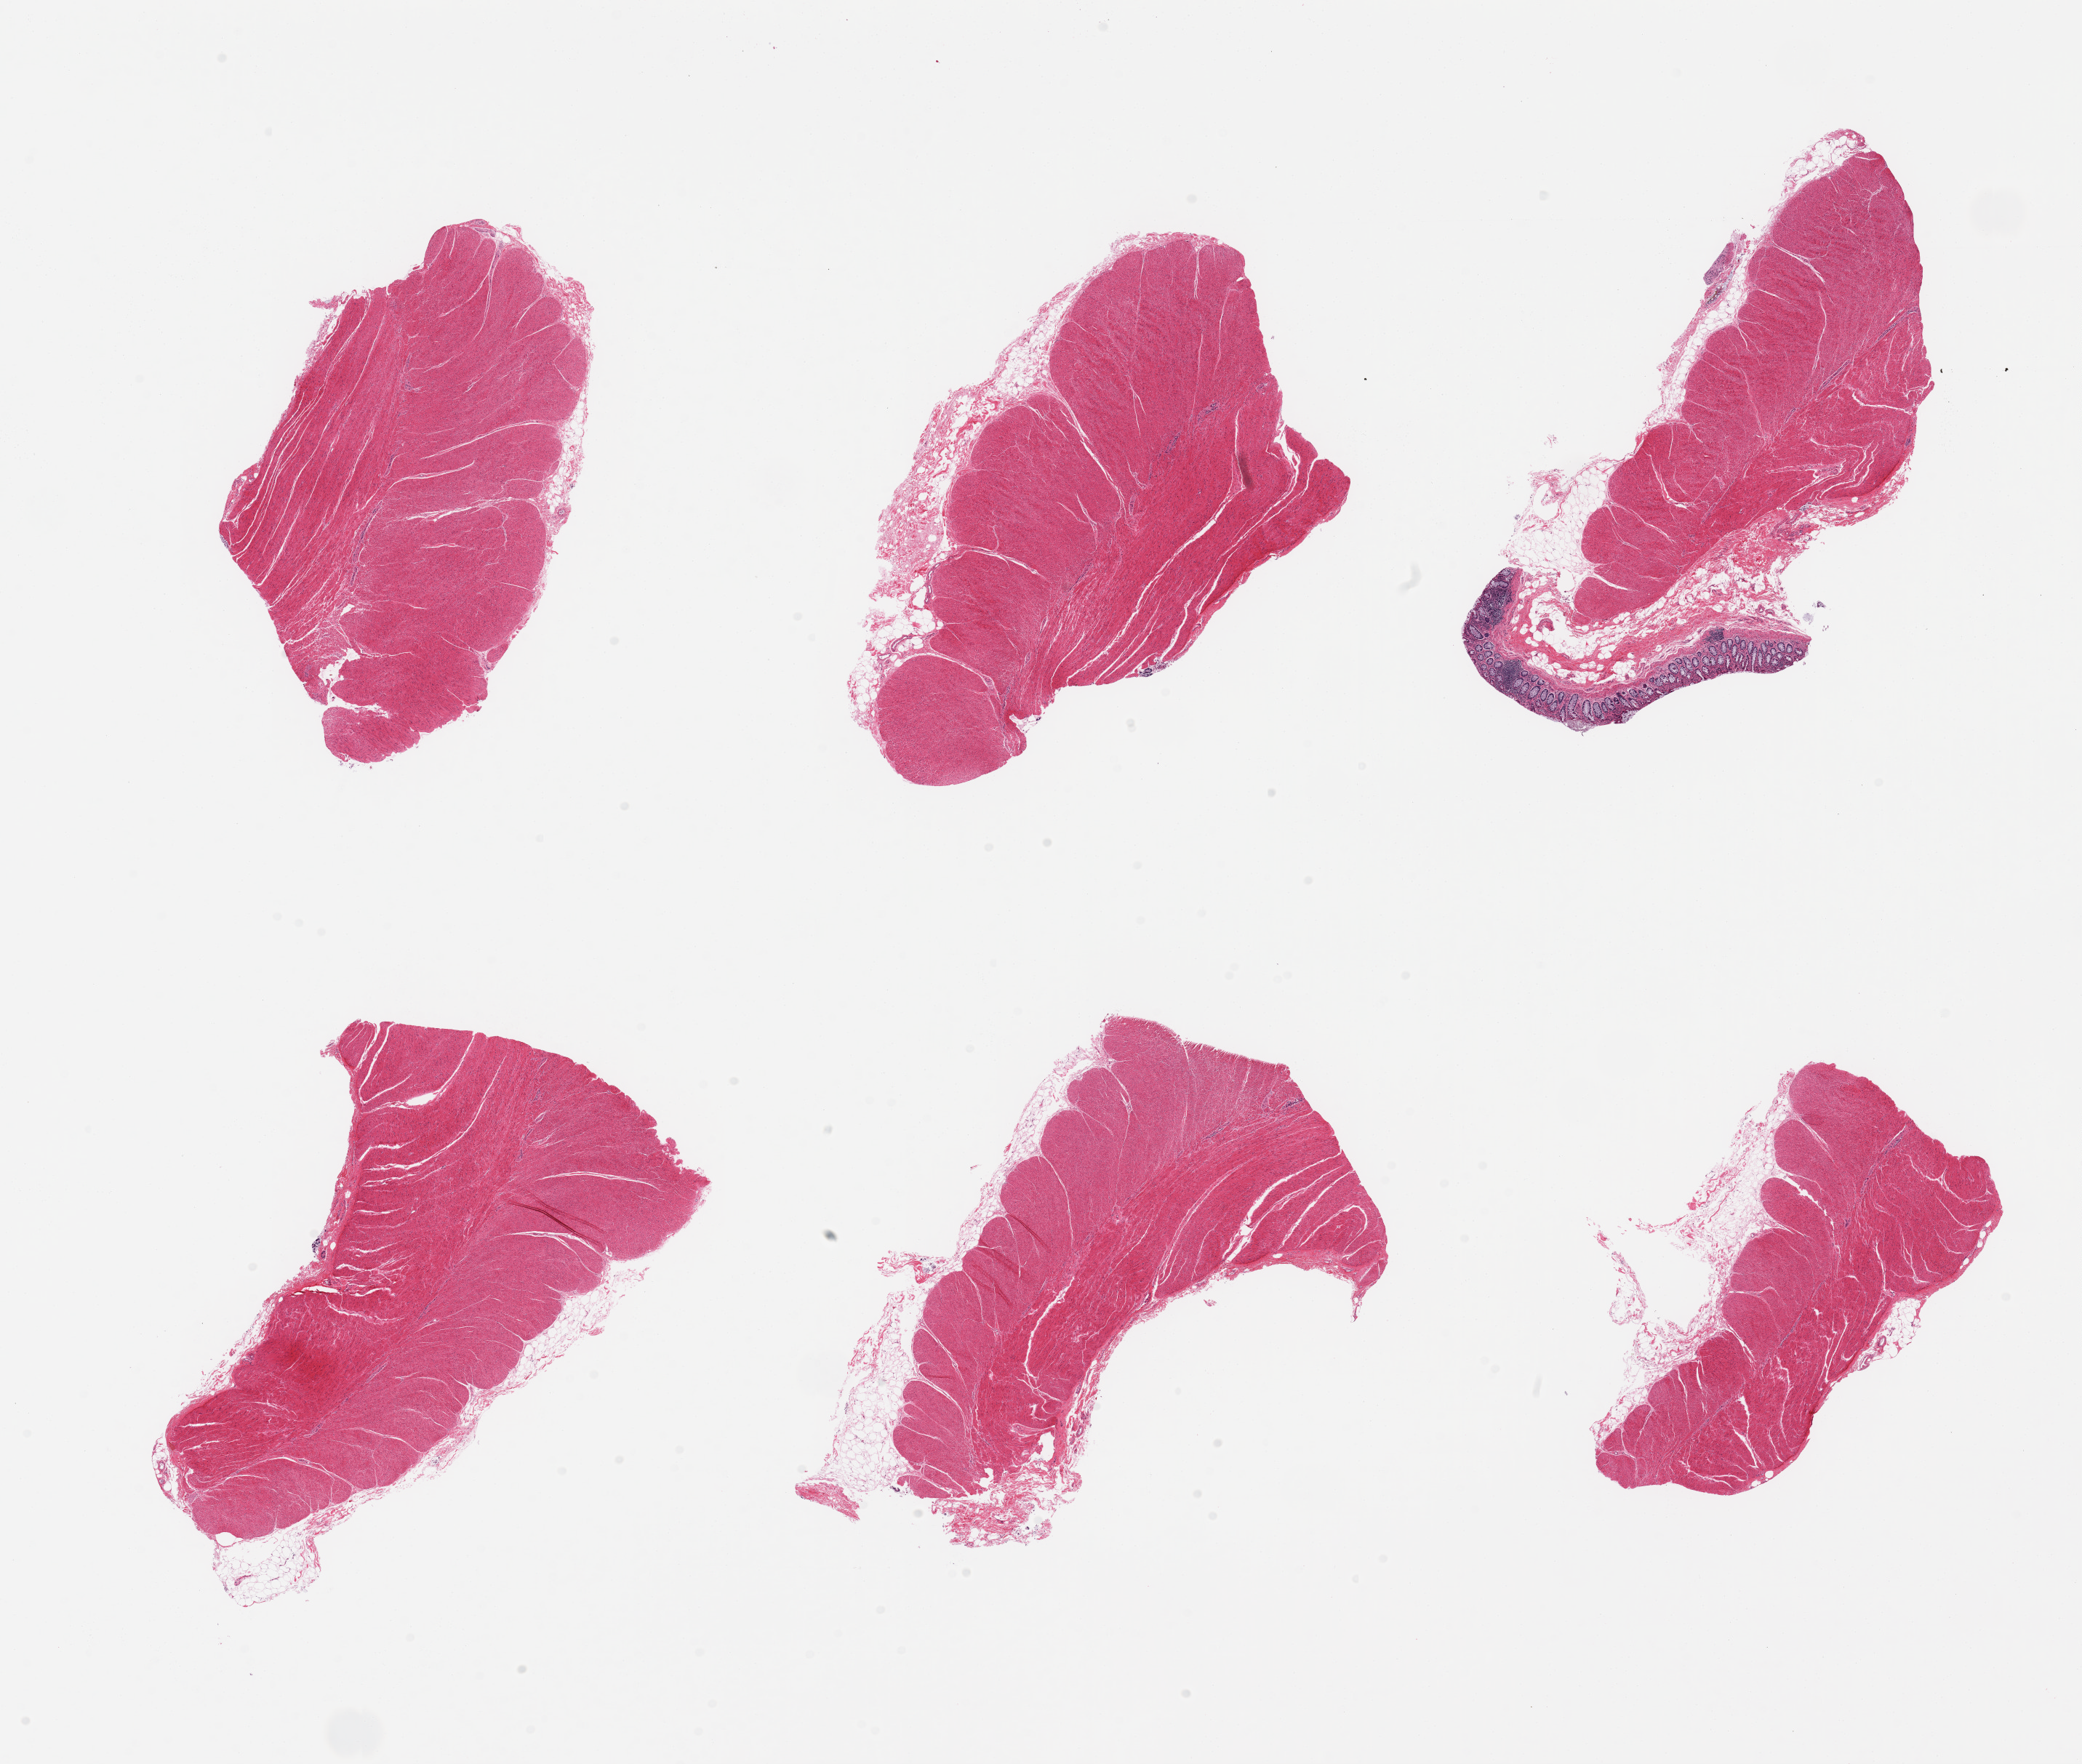
Digitized H&E-stained section, brightfield — a low-resolution overview of the entire scanned area, about 22.6 x 19.2 mm (acquisition: 20x scan), PAXgene-fixed paraffin-embedded (PFPE) section, target tissue: sigmoid colon, donor tissue sample. Donor: male.
Review note (as recorded): 6 pieces, target muscularis; trace adherent fat, trace autolyzed mucosa.